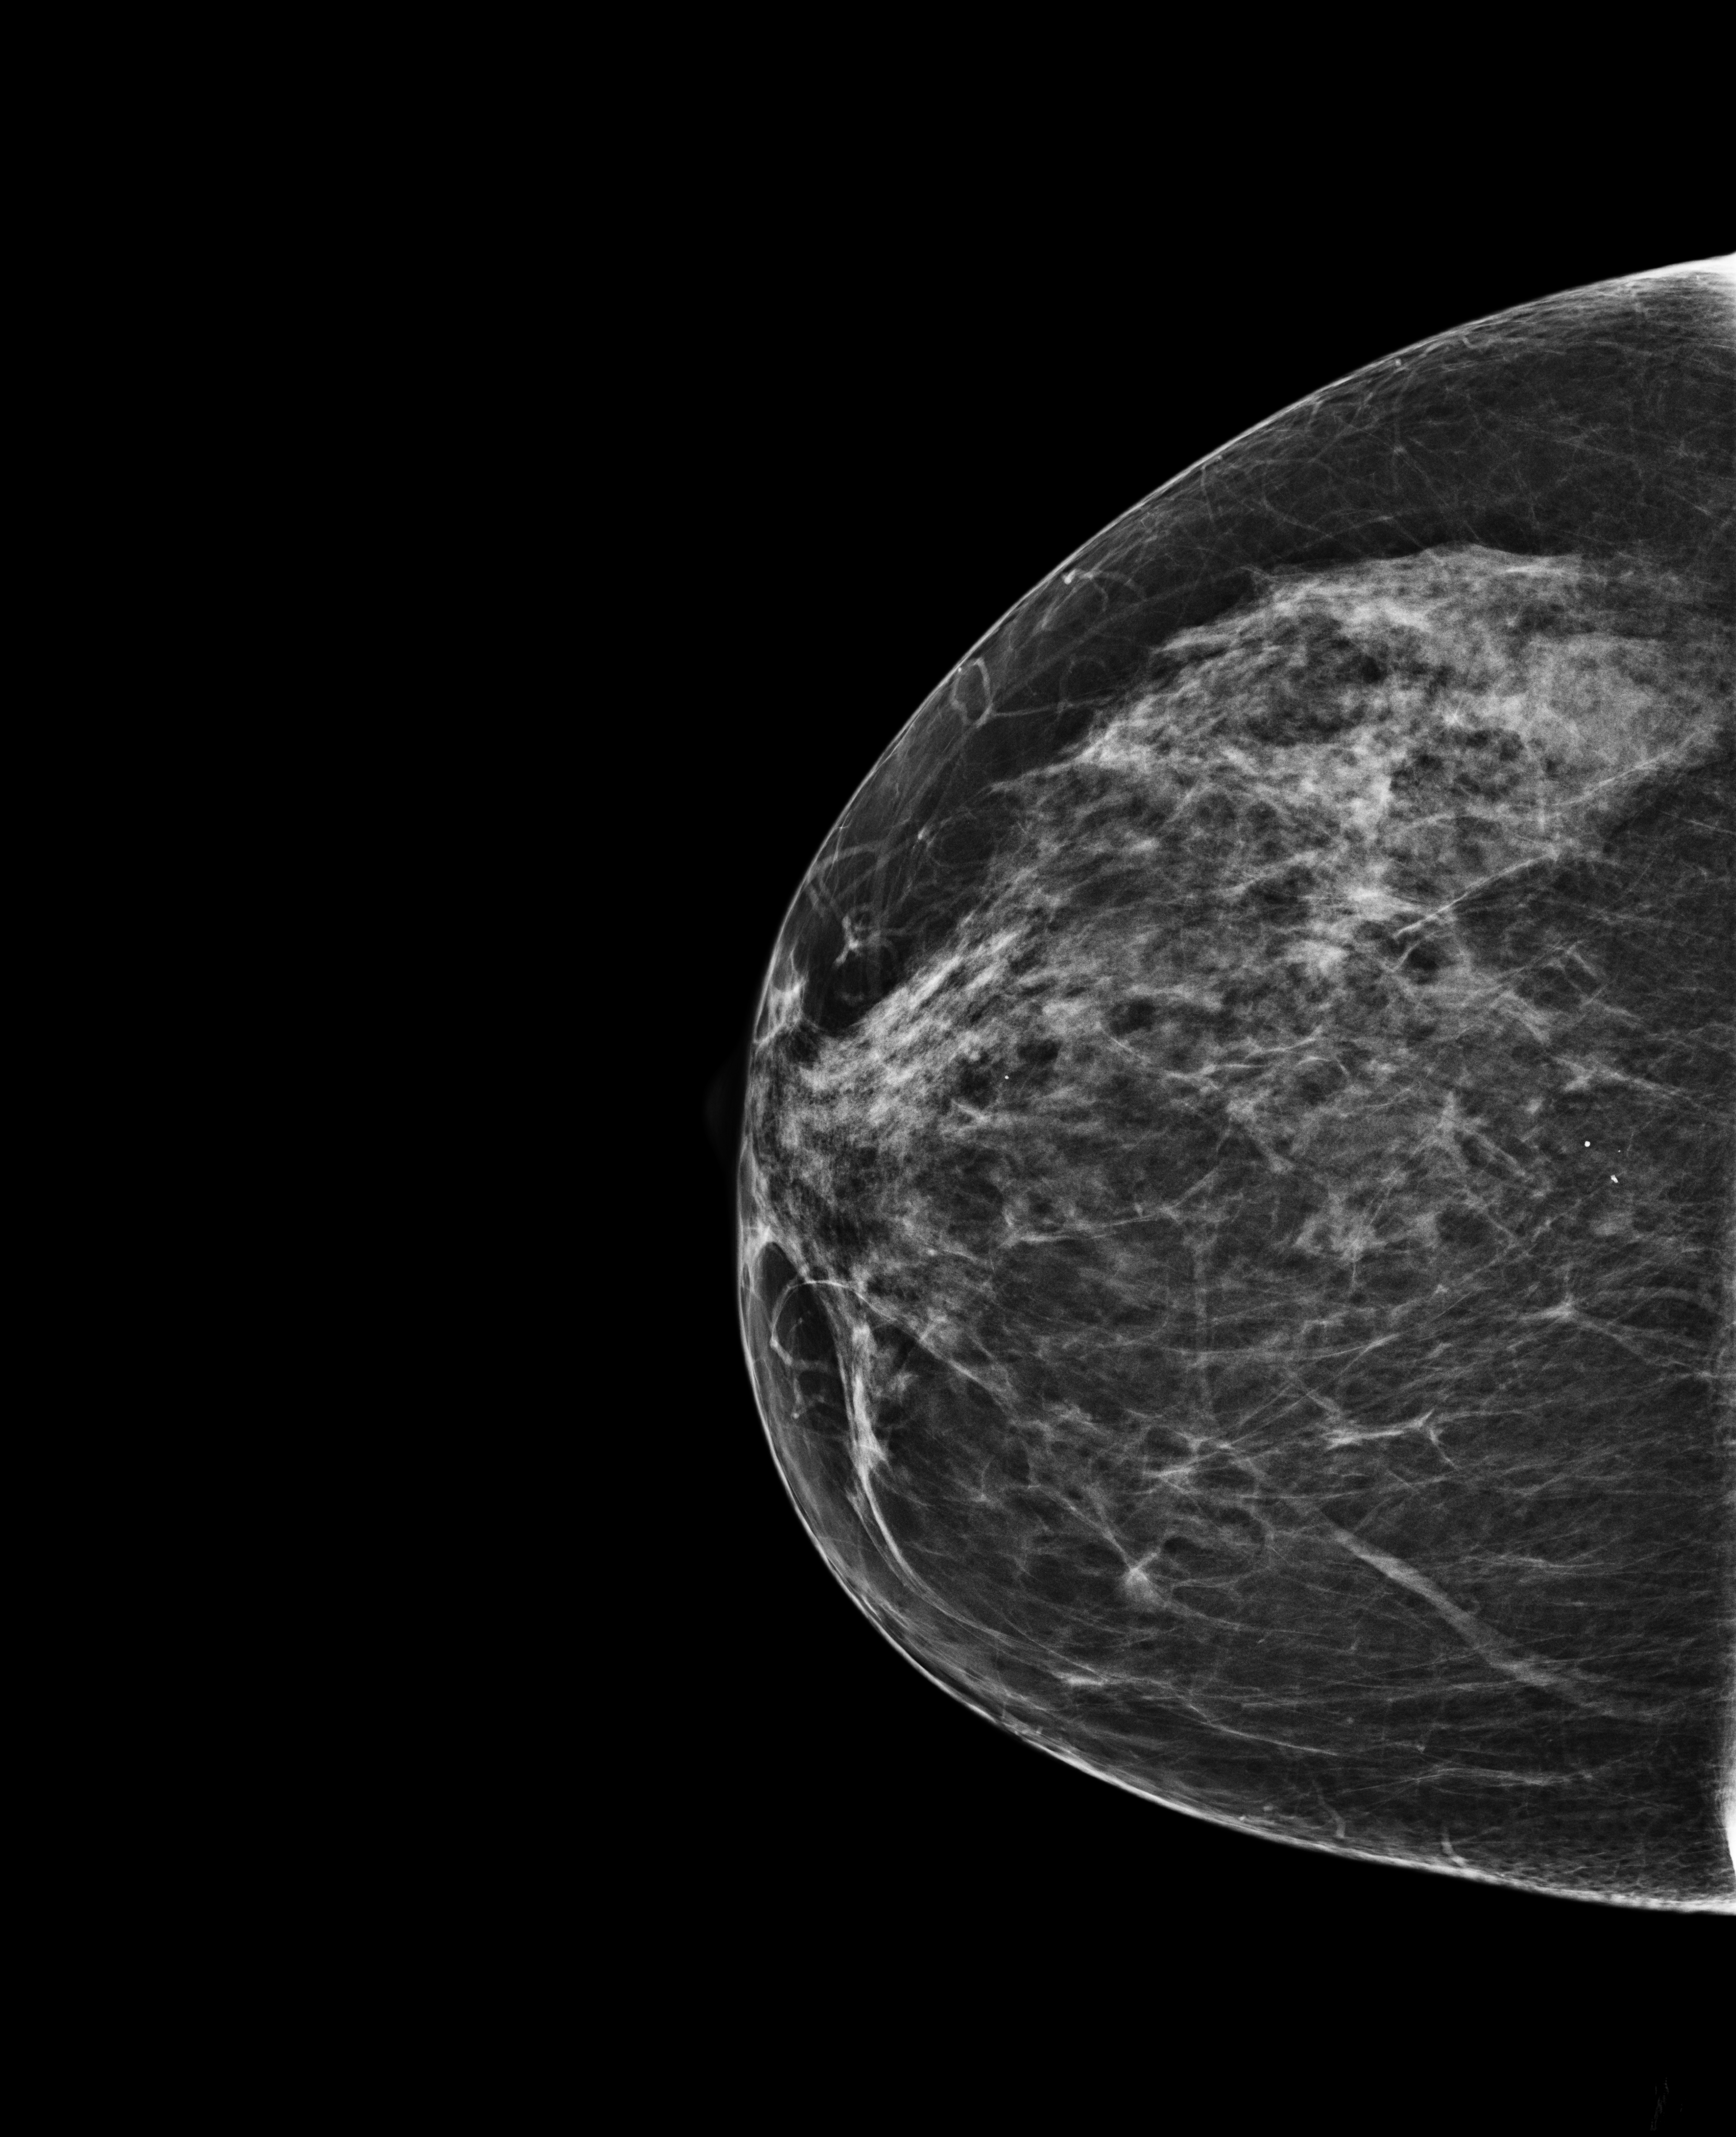
Full-field digital mammogram (FFDM); right breast; CC view; screening examination; system: Selenia Dimensions. Patient aged 58 years (female).
Final BI-RADS category for the screening round (tomosynthesis exam, both breasts): category 1.